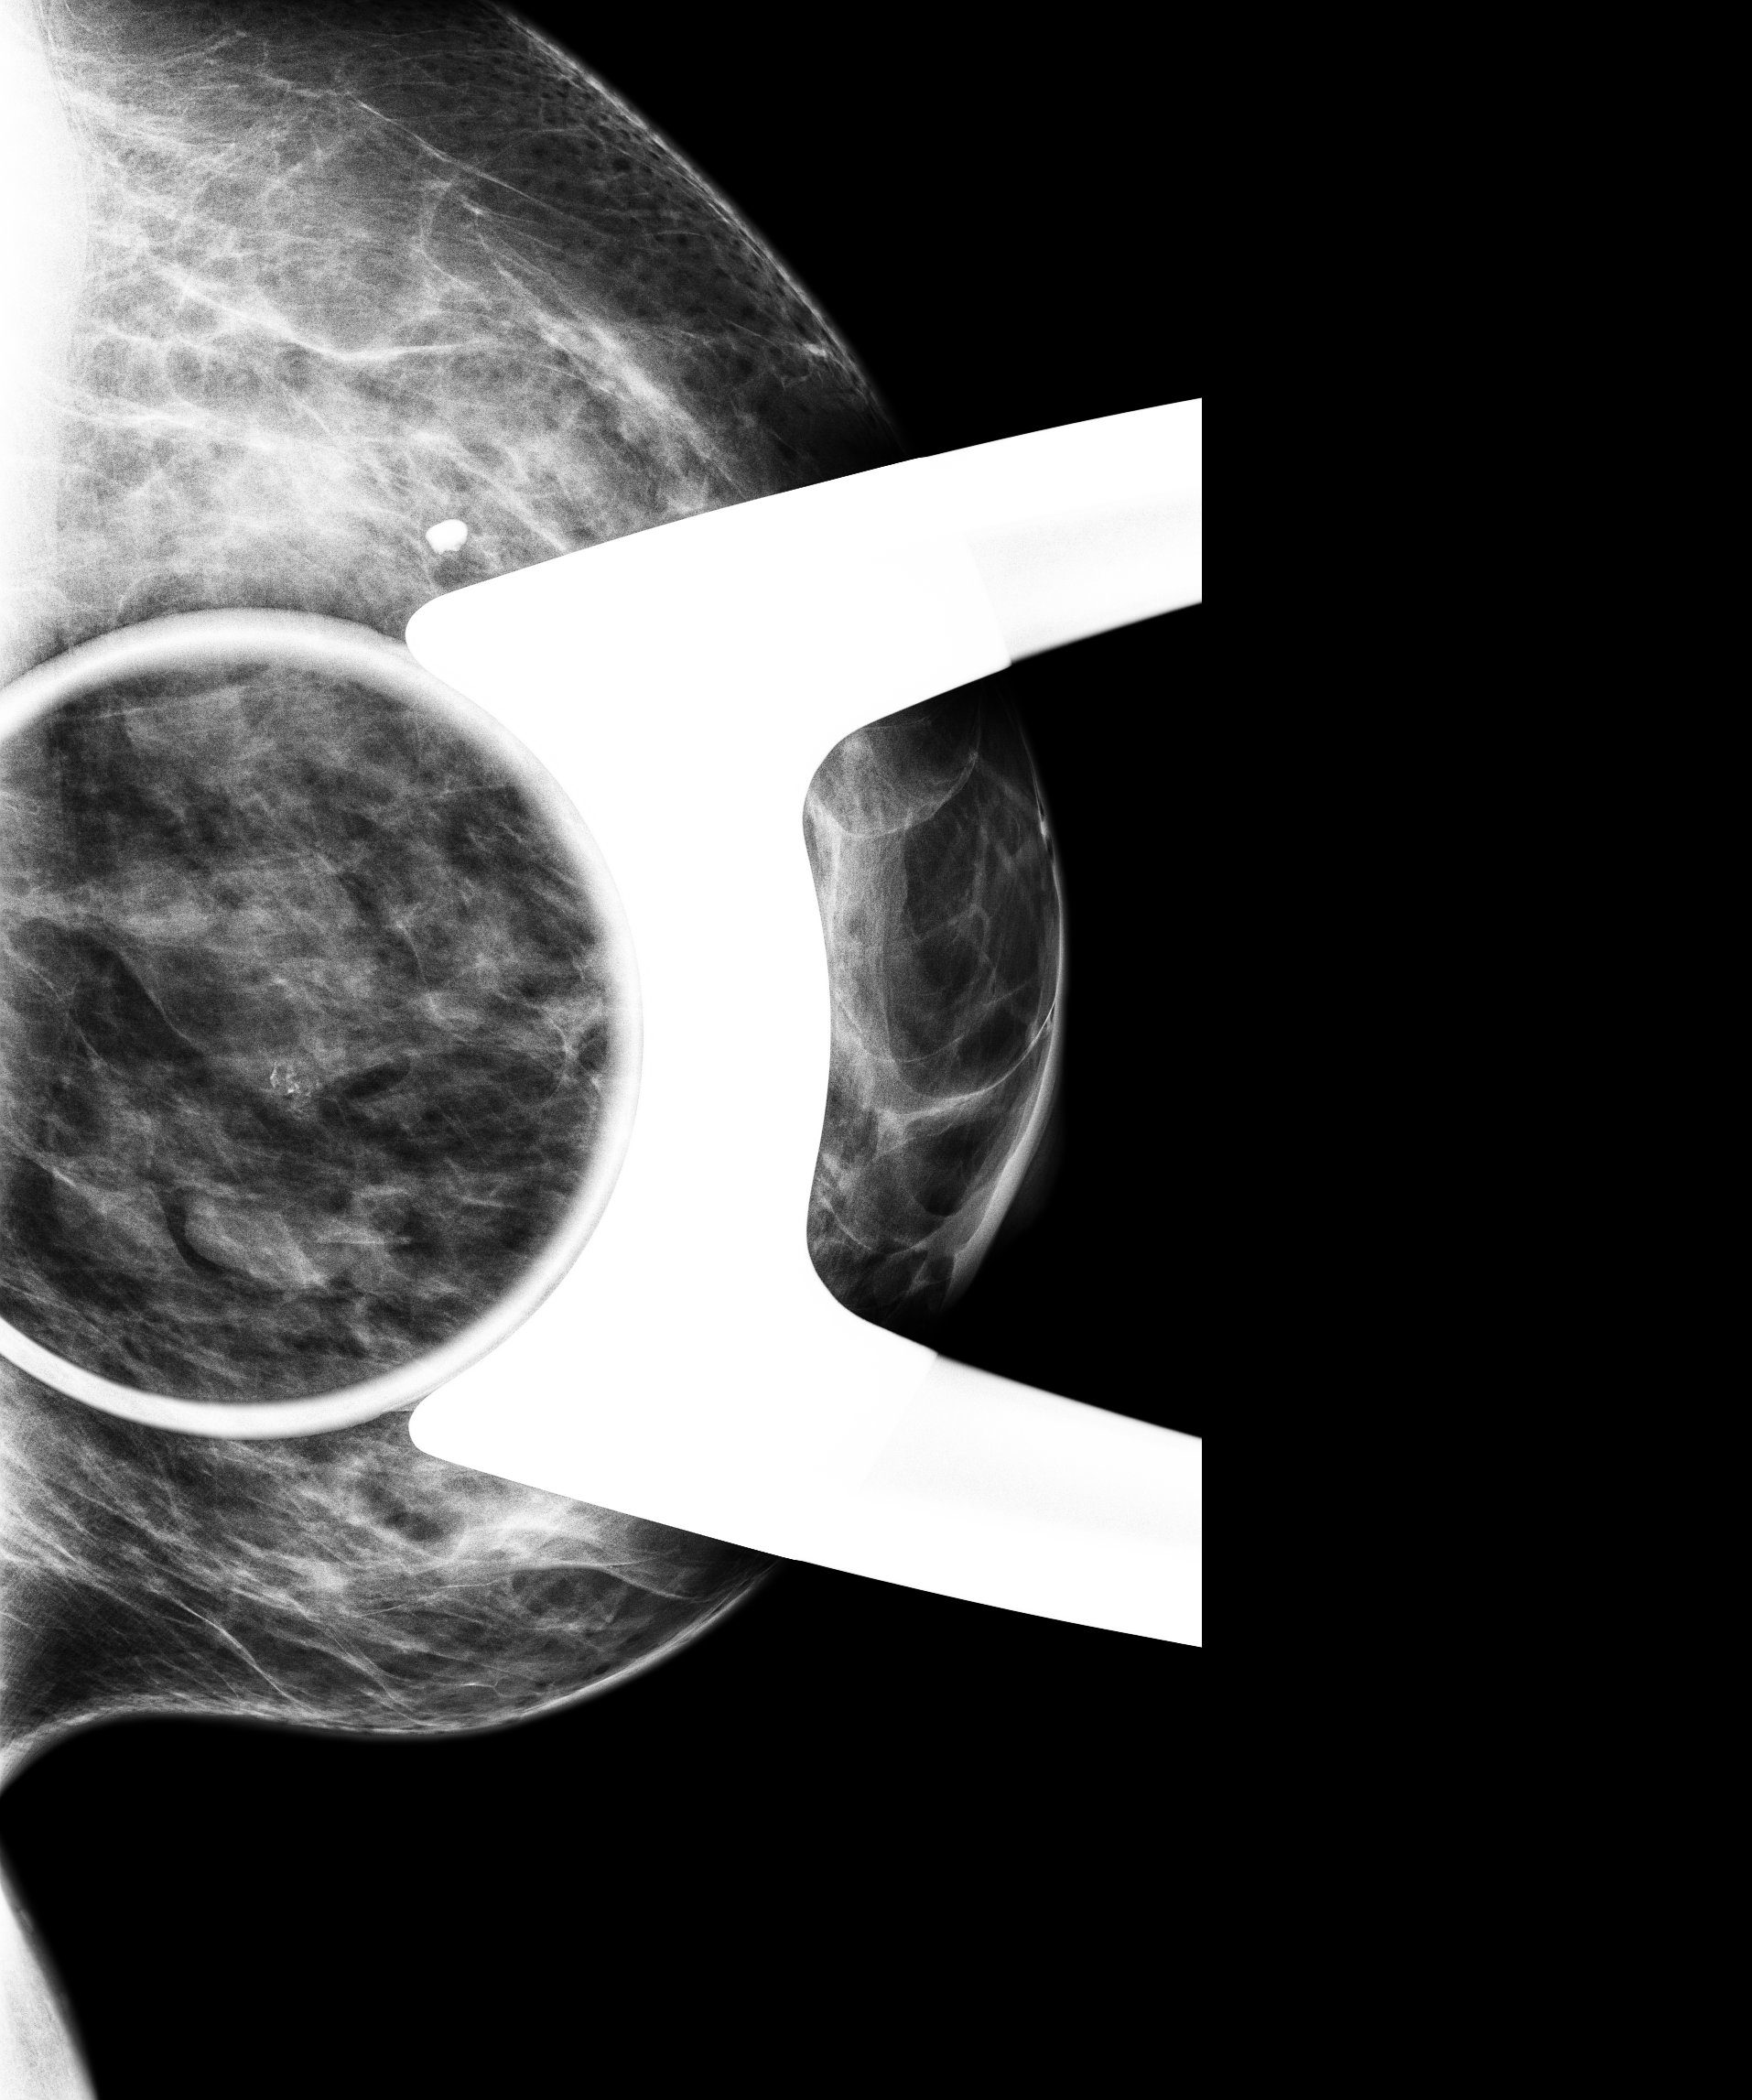
Diagnostic examination (additional views). Patient: female, 52 years.
Image type: full-field digital mammogram. Breast: left. Projection: lateromedial (LM) view.